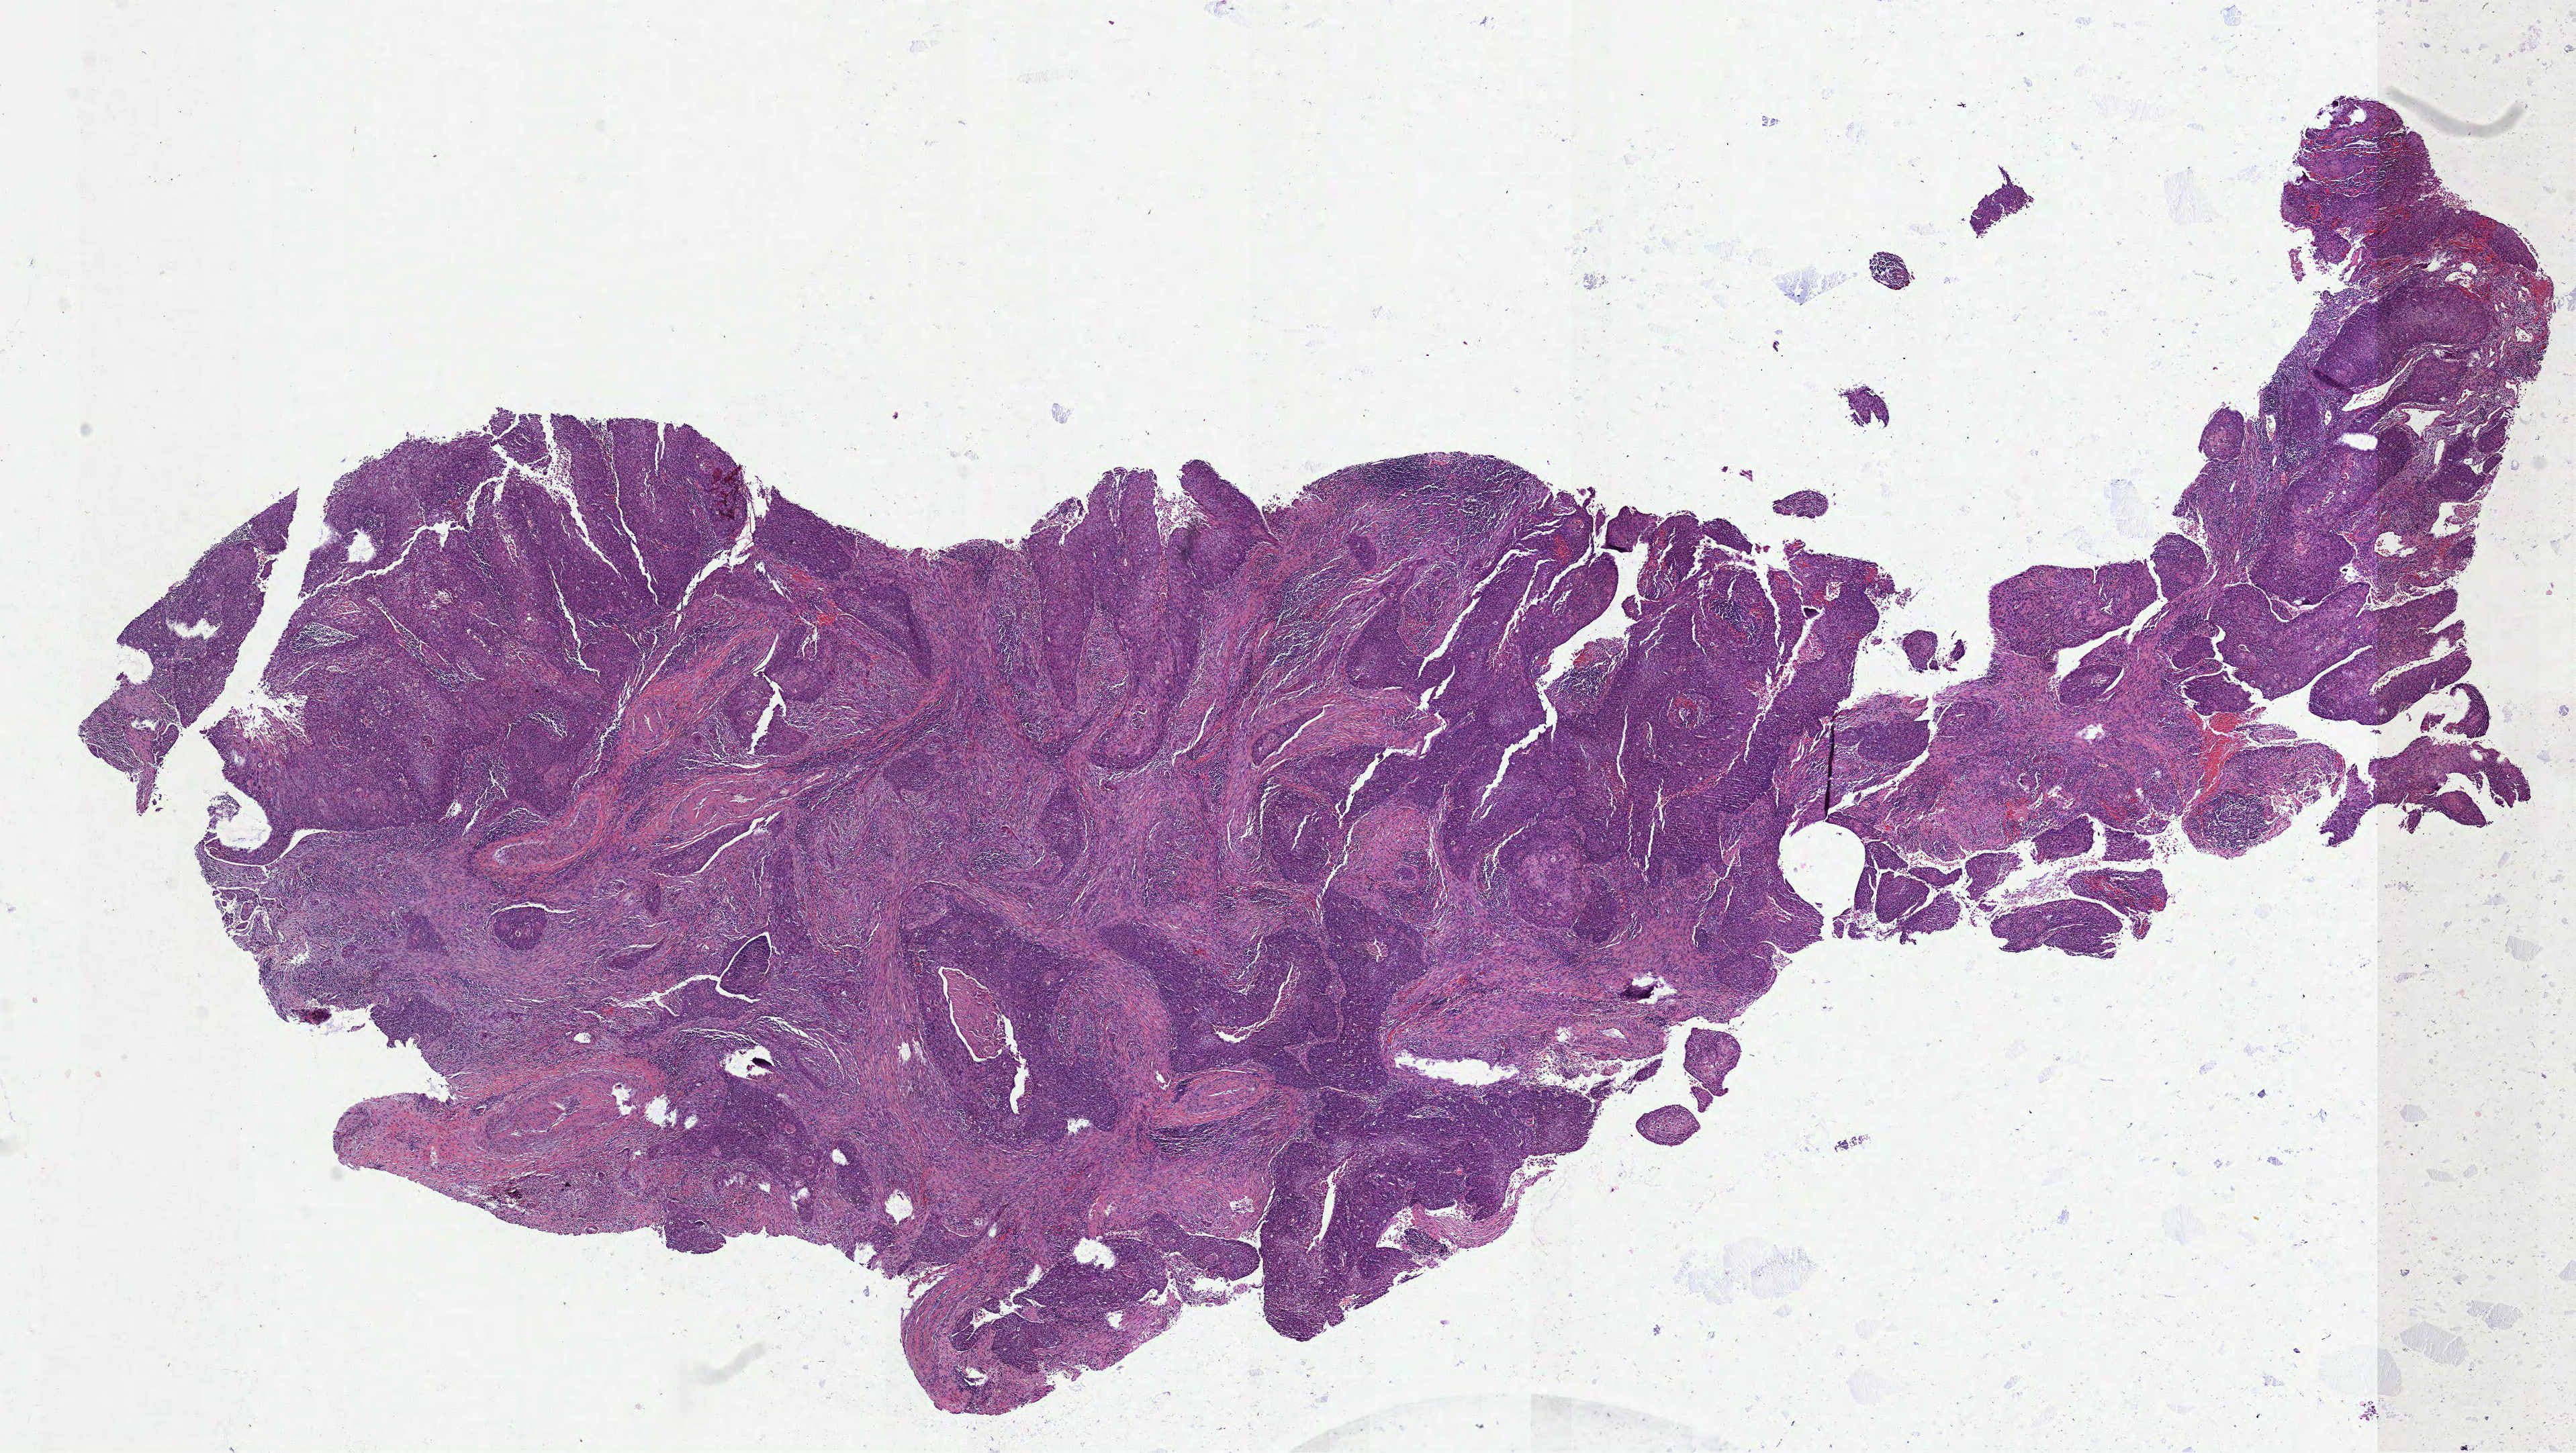
Digitized H&E-stained tissue section (whole slide), whole scanned area (about 15.5 x 8.7 mm, acquisition: 40x scan) shown as a low-resolution overview, formalin-fixed paraffin-embedded (FFPE) diagnostic section, sample: primary tumour, cervix. Patient: female, age at initial diagnosis 55 years. Histologic grade: G2 (moderately differentiated).
FIGO stage: IIIB. Histologic diagnosis: Squamous cell carcinoma, NOS.